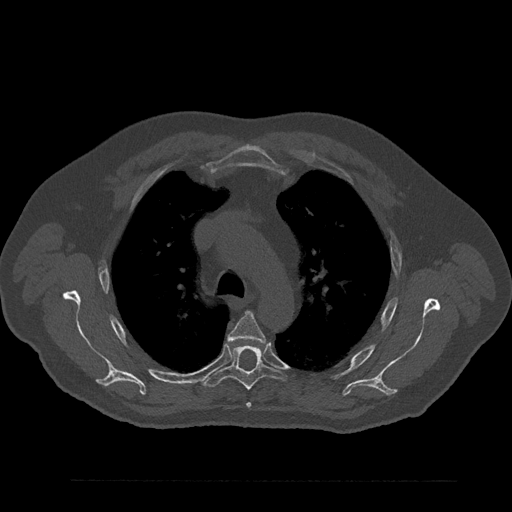
CT including the spine, one axial slice; slice 615 of 797 in the series (ordered by position); reconstruction kernel Br40s/3; bone window (W 1800 / L 400 HU); 512 × 512 image matrix, field of view 430 × 430 mm. Patient: male, 61 years. Case-level facts recorded for this patient, not image findings: primary cancer: prostate.
Outlined on this slice (semi-automatic segmentation, software-assisted and operator-edited):
- T4 vertebra: box from (x=227, y=311) to (x=266, y=408) px
- T5 vertebra: (x=203, y=345)–(x=287, y=391)